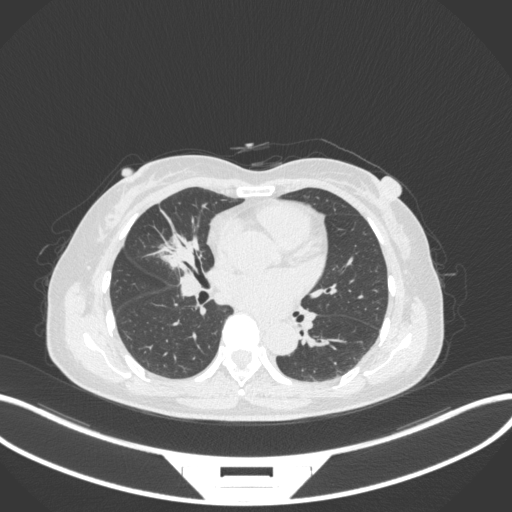
Chest CT, one axial slice. Position 149 of 282 along the scan axis. Reconstruction kernel B31f. 120 kVp. Lung window (W 1500 / L -600 HU). 1 mm slice thickness. 512 × 512 image matrix, field of view 400 × 400 mm. Patient: female, 51 years. From the clinical record (not read from this slice): clinical TNM (as recorded): T1c N0 M0.
Outlined on this slice (rectangle marked by the reading radiologist):
- lung tumour (recorded histology: adenocarcinoma): bounding box (x1, y1, x2, y2) in pixels: (151, 227, 205, 273)